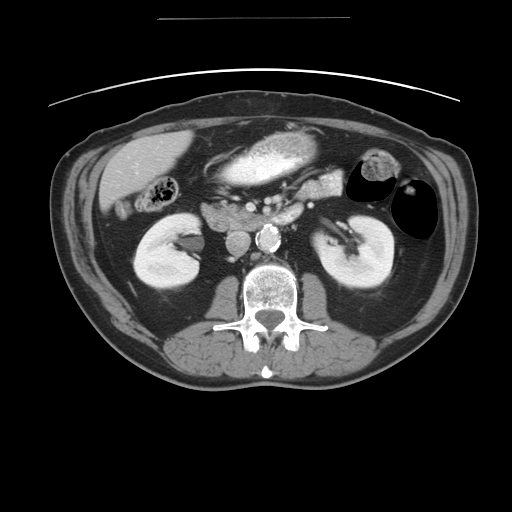
Contrast-enhanced abdominal CT, one axial slice. Slice 15 of 49 in the series (ordered by position). Reconstruction kernel STANDARD. Intravenous contrast given. Soft-tissue window (W 400 / L 40 HU). 5 mm slice thickness. 512 × 512 image matrix, field of view 413 × 413 mm. Male patient, age 57 years. From the clinical record (not read from this slice): diagnosis: colorectal cancer liver metastases, imaged before liver resection; multiple liver metastases: yes; largest metastasis: 4 cm; disease in both lobes: no.
Annotated regions visible in this slice (manually delineated by an expert):
- liver: bounding box <99,131,191,207> (left, top, right, bottom; pixels)